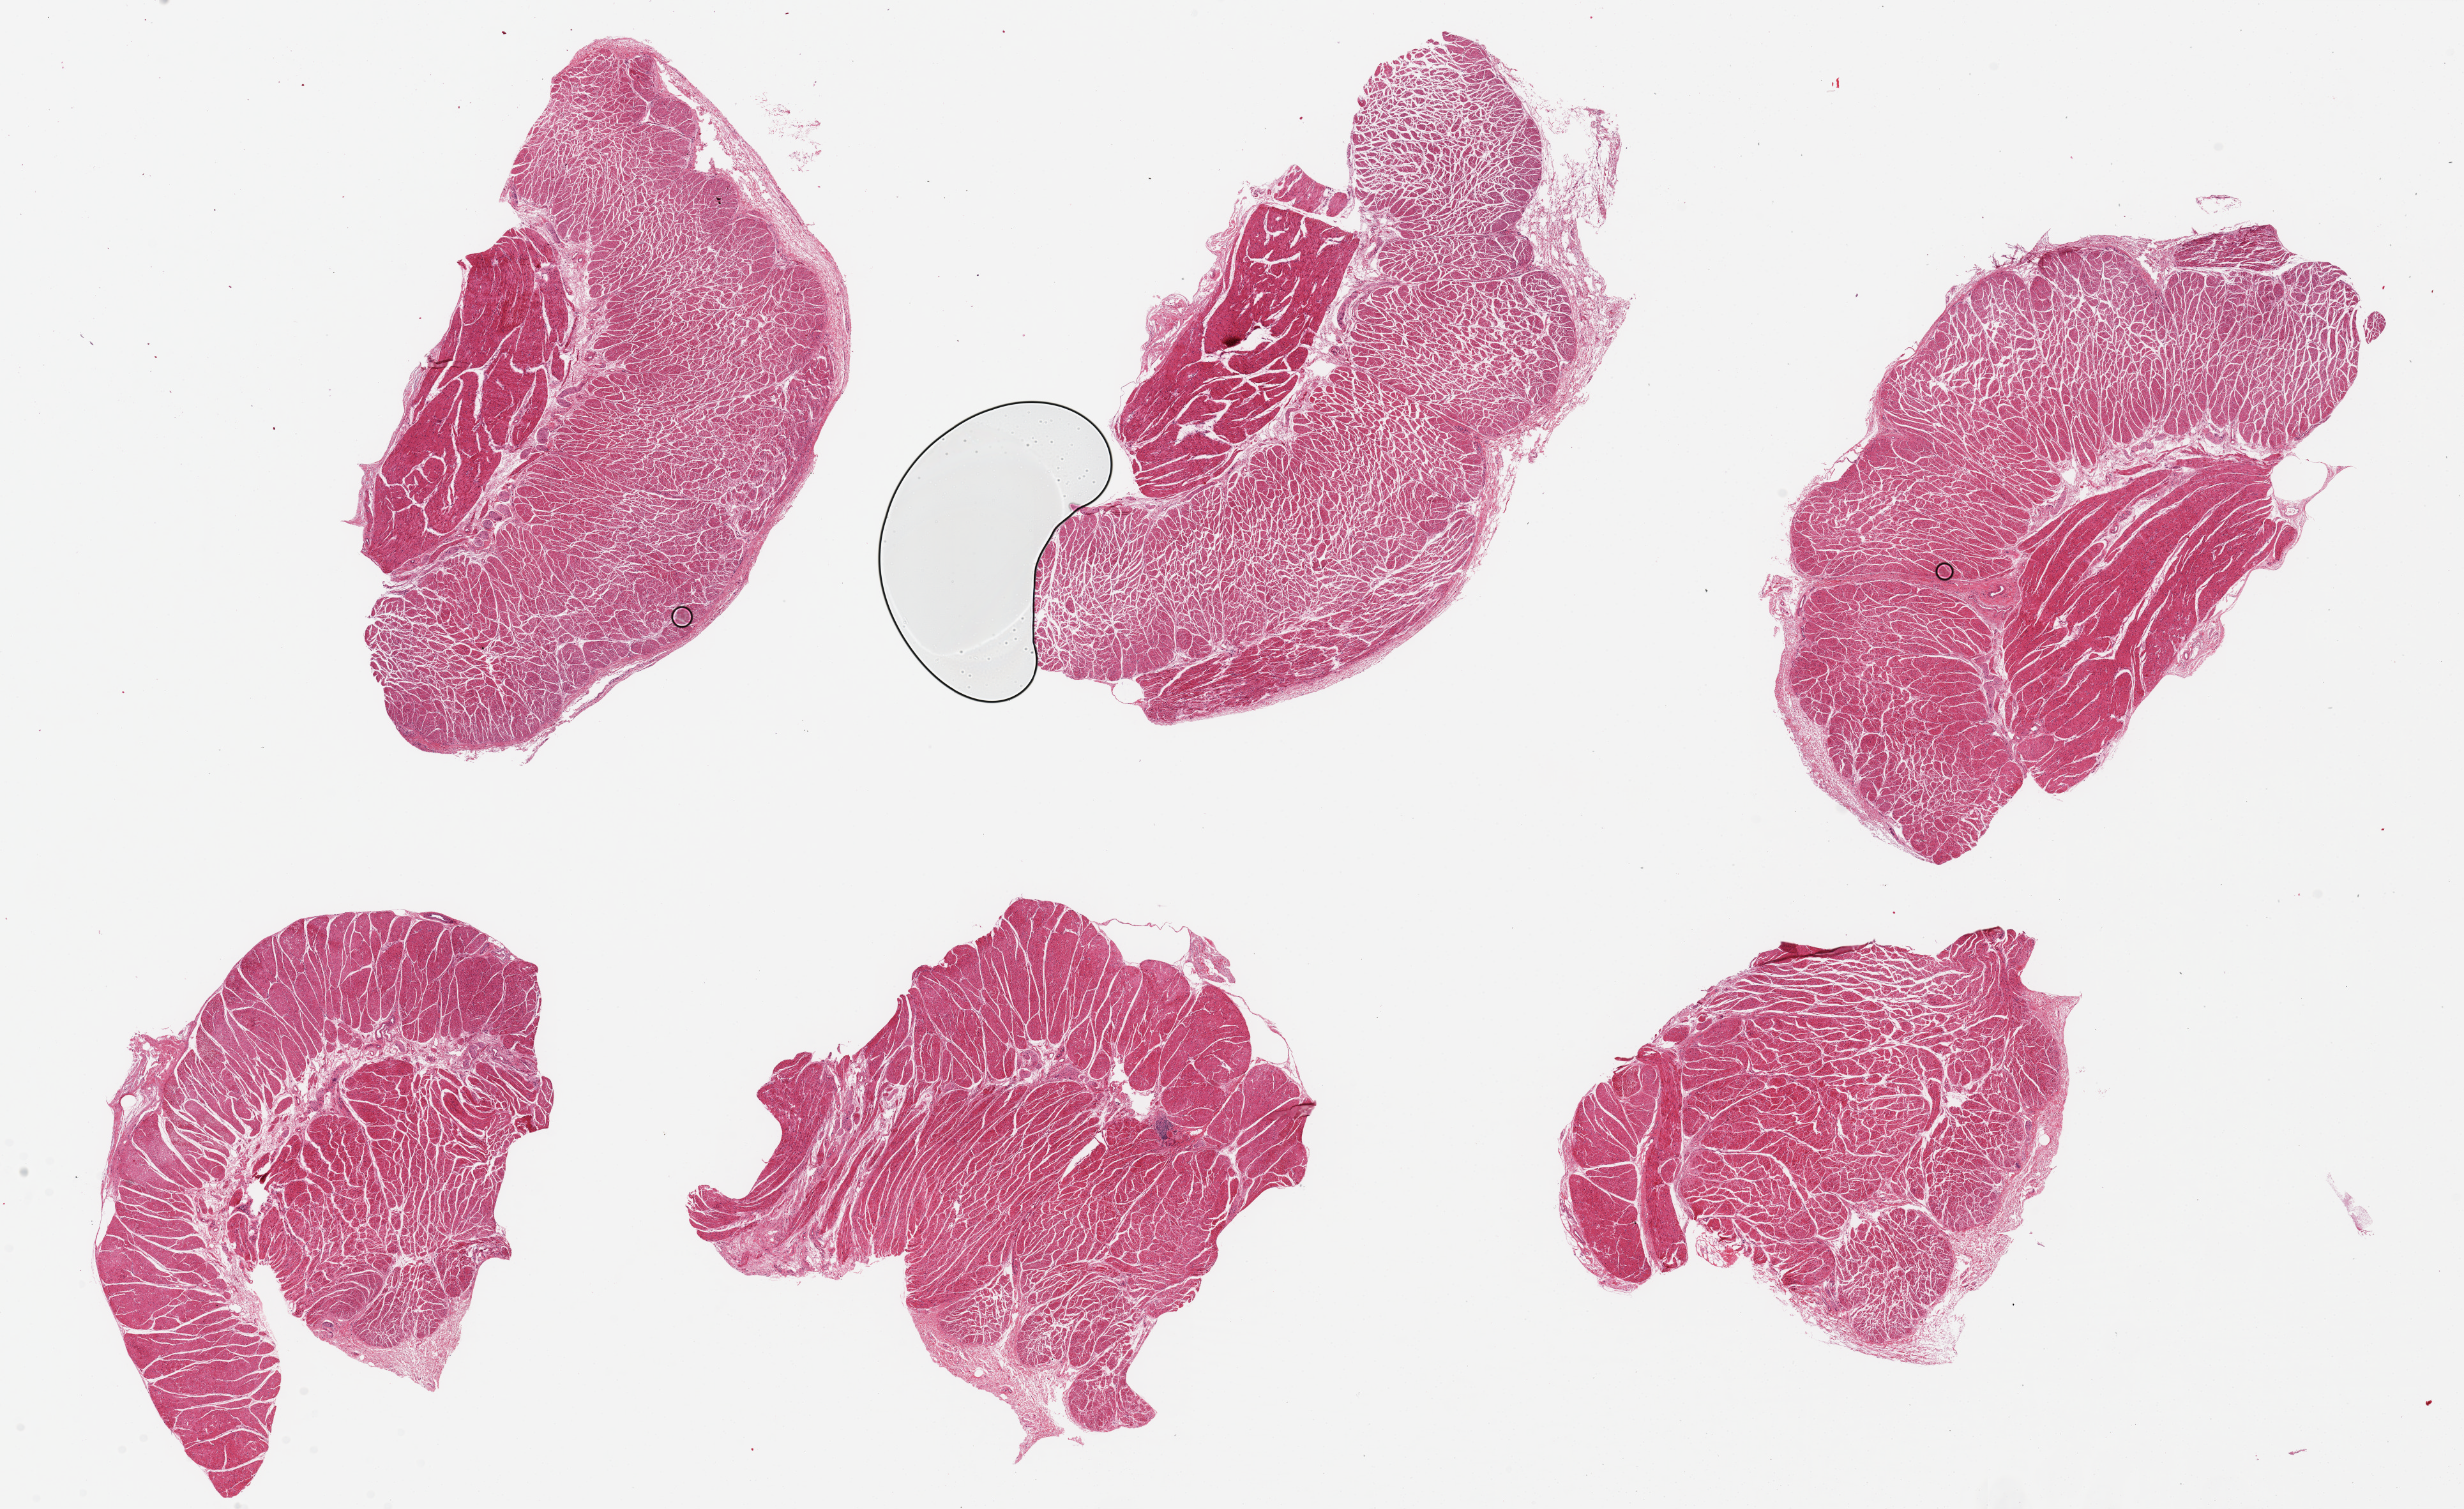
H&E whole-slide image, low-resolution overview of the scanned area, about 30.5 x 18.7 mm (slide scanned at 20x); PAXgene-fixed paraffin-embedded (PFPE) section; target tissue: esophageal muscle; donor tissue sample. Male donor.
Pathologist's review note for this sample: 6 ~9x4 mm pieces.